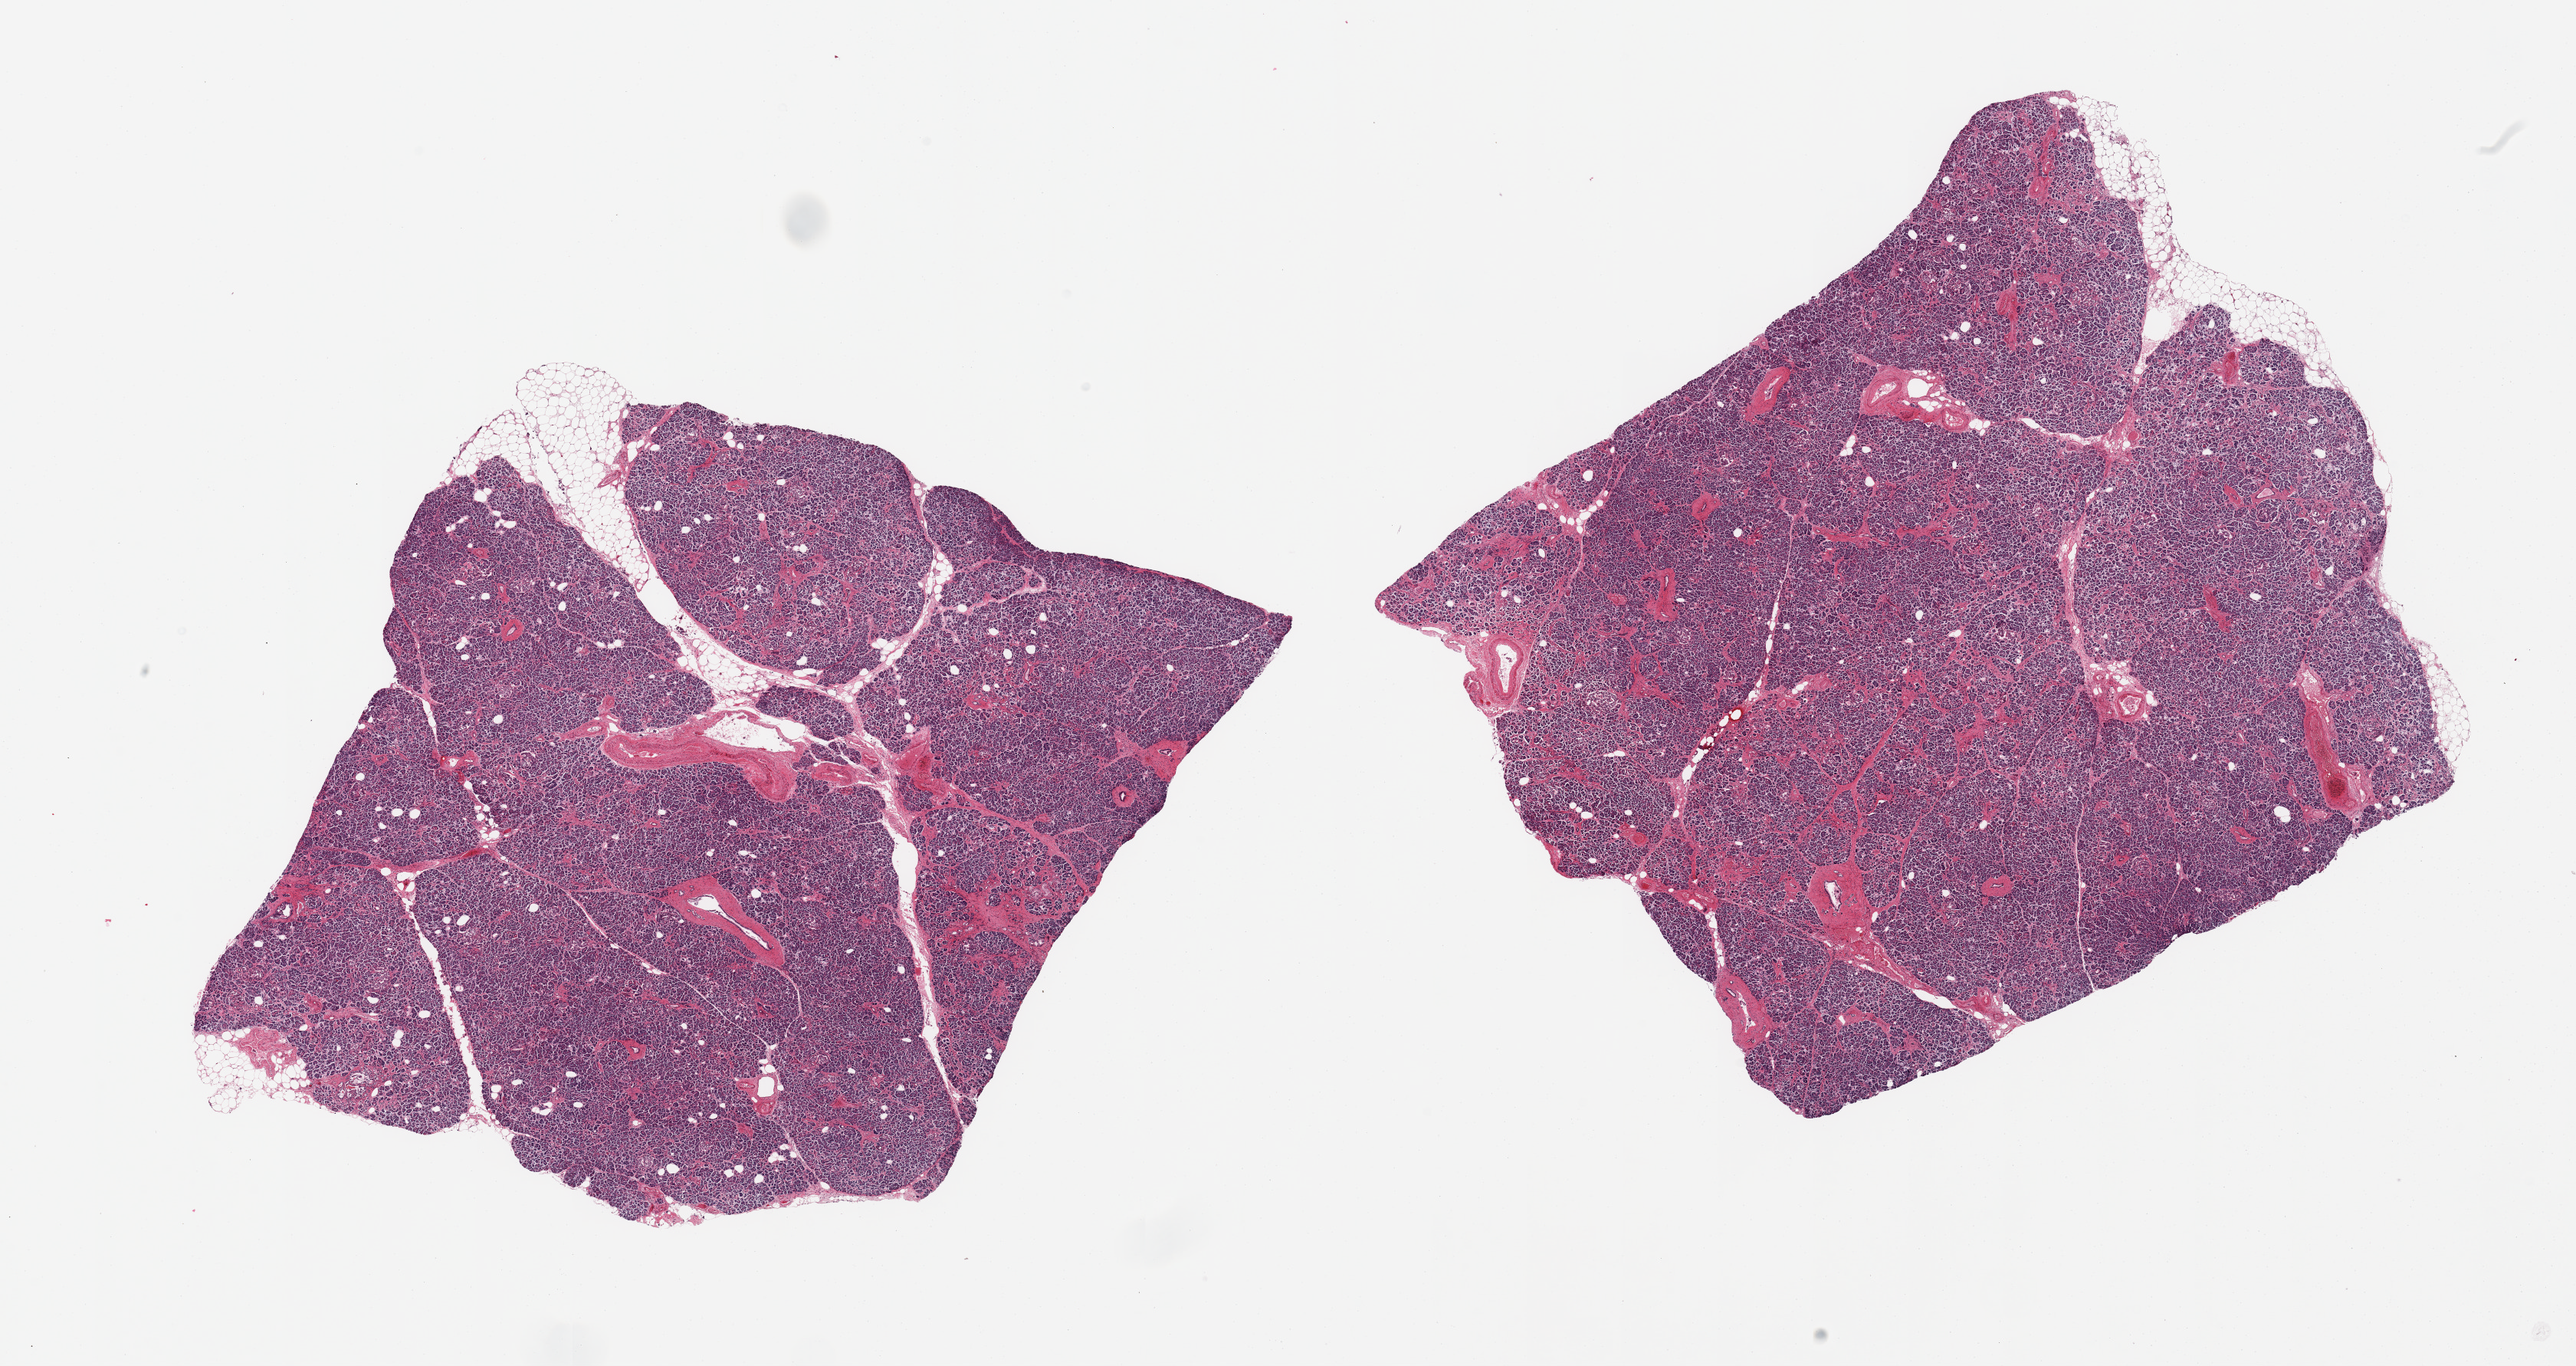
H&E whole-slide image, brightfield — shown as a low-resolution overview of the whole scanned area (about 26.6 x 14.1 mm); PAXgene-fixed paraffin-embedded (PFPE) section; sampled site (target tissue): pancreas; donor tissue sample. Female donor.
Reviewer comment on this tissue sample: 2 pieces; 5% fat.